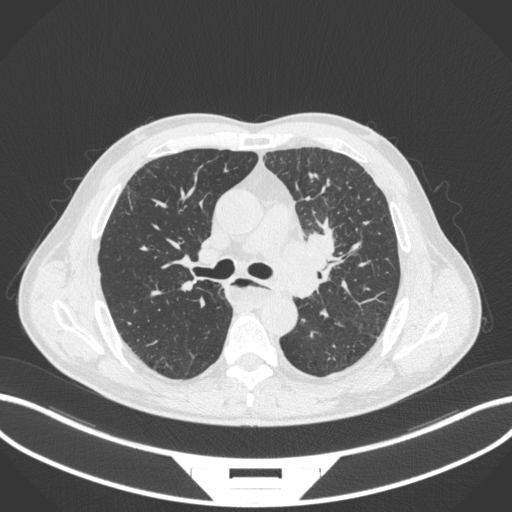
Chest CT, one axial slice. Lung window (W 1500 / L -600 HU). 1 mm slice thickness. 512 × 512 image matrix, field of view 400 × 400 mm. Patient: male, 57 years. Case-level facts recorded for this patient, not image findings: clinical TNM (as recorded): T2a N1 M0.
Annotated regions visible in this slice (bounding box drawn by a radiologist):
- lung tumour (recorded histology: squamous cell carcinoma): bounding box (x1, y1, x2, y2) in pixels: (283, 215, 346, 302)